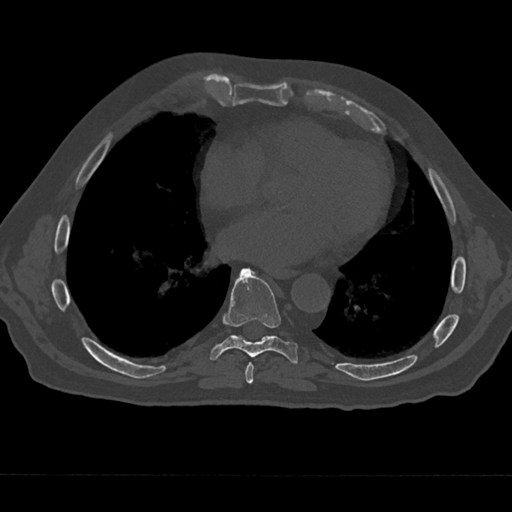
CT including the spine, one axial slice; position 316 of 797 along the scan axis; reconstruction kernel Br40s/3; bone window (W 1800 / L 400 HU); 0.5 mm slice thickness; 512 × 512 image matrix. Patient: male, 75 years. Case-level facts recorded for this patient, not image findings: primary cancer: renal; vertebrae with lytic lesions (as recorded): T4.
Structures marked on this image (semi-automatically segmented with operator editing):
- T7 vertebra: bounding box <241,362,259,384> (left, top, right, bottom; pixels)
- T8 vertebra: <210,269,298,364>